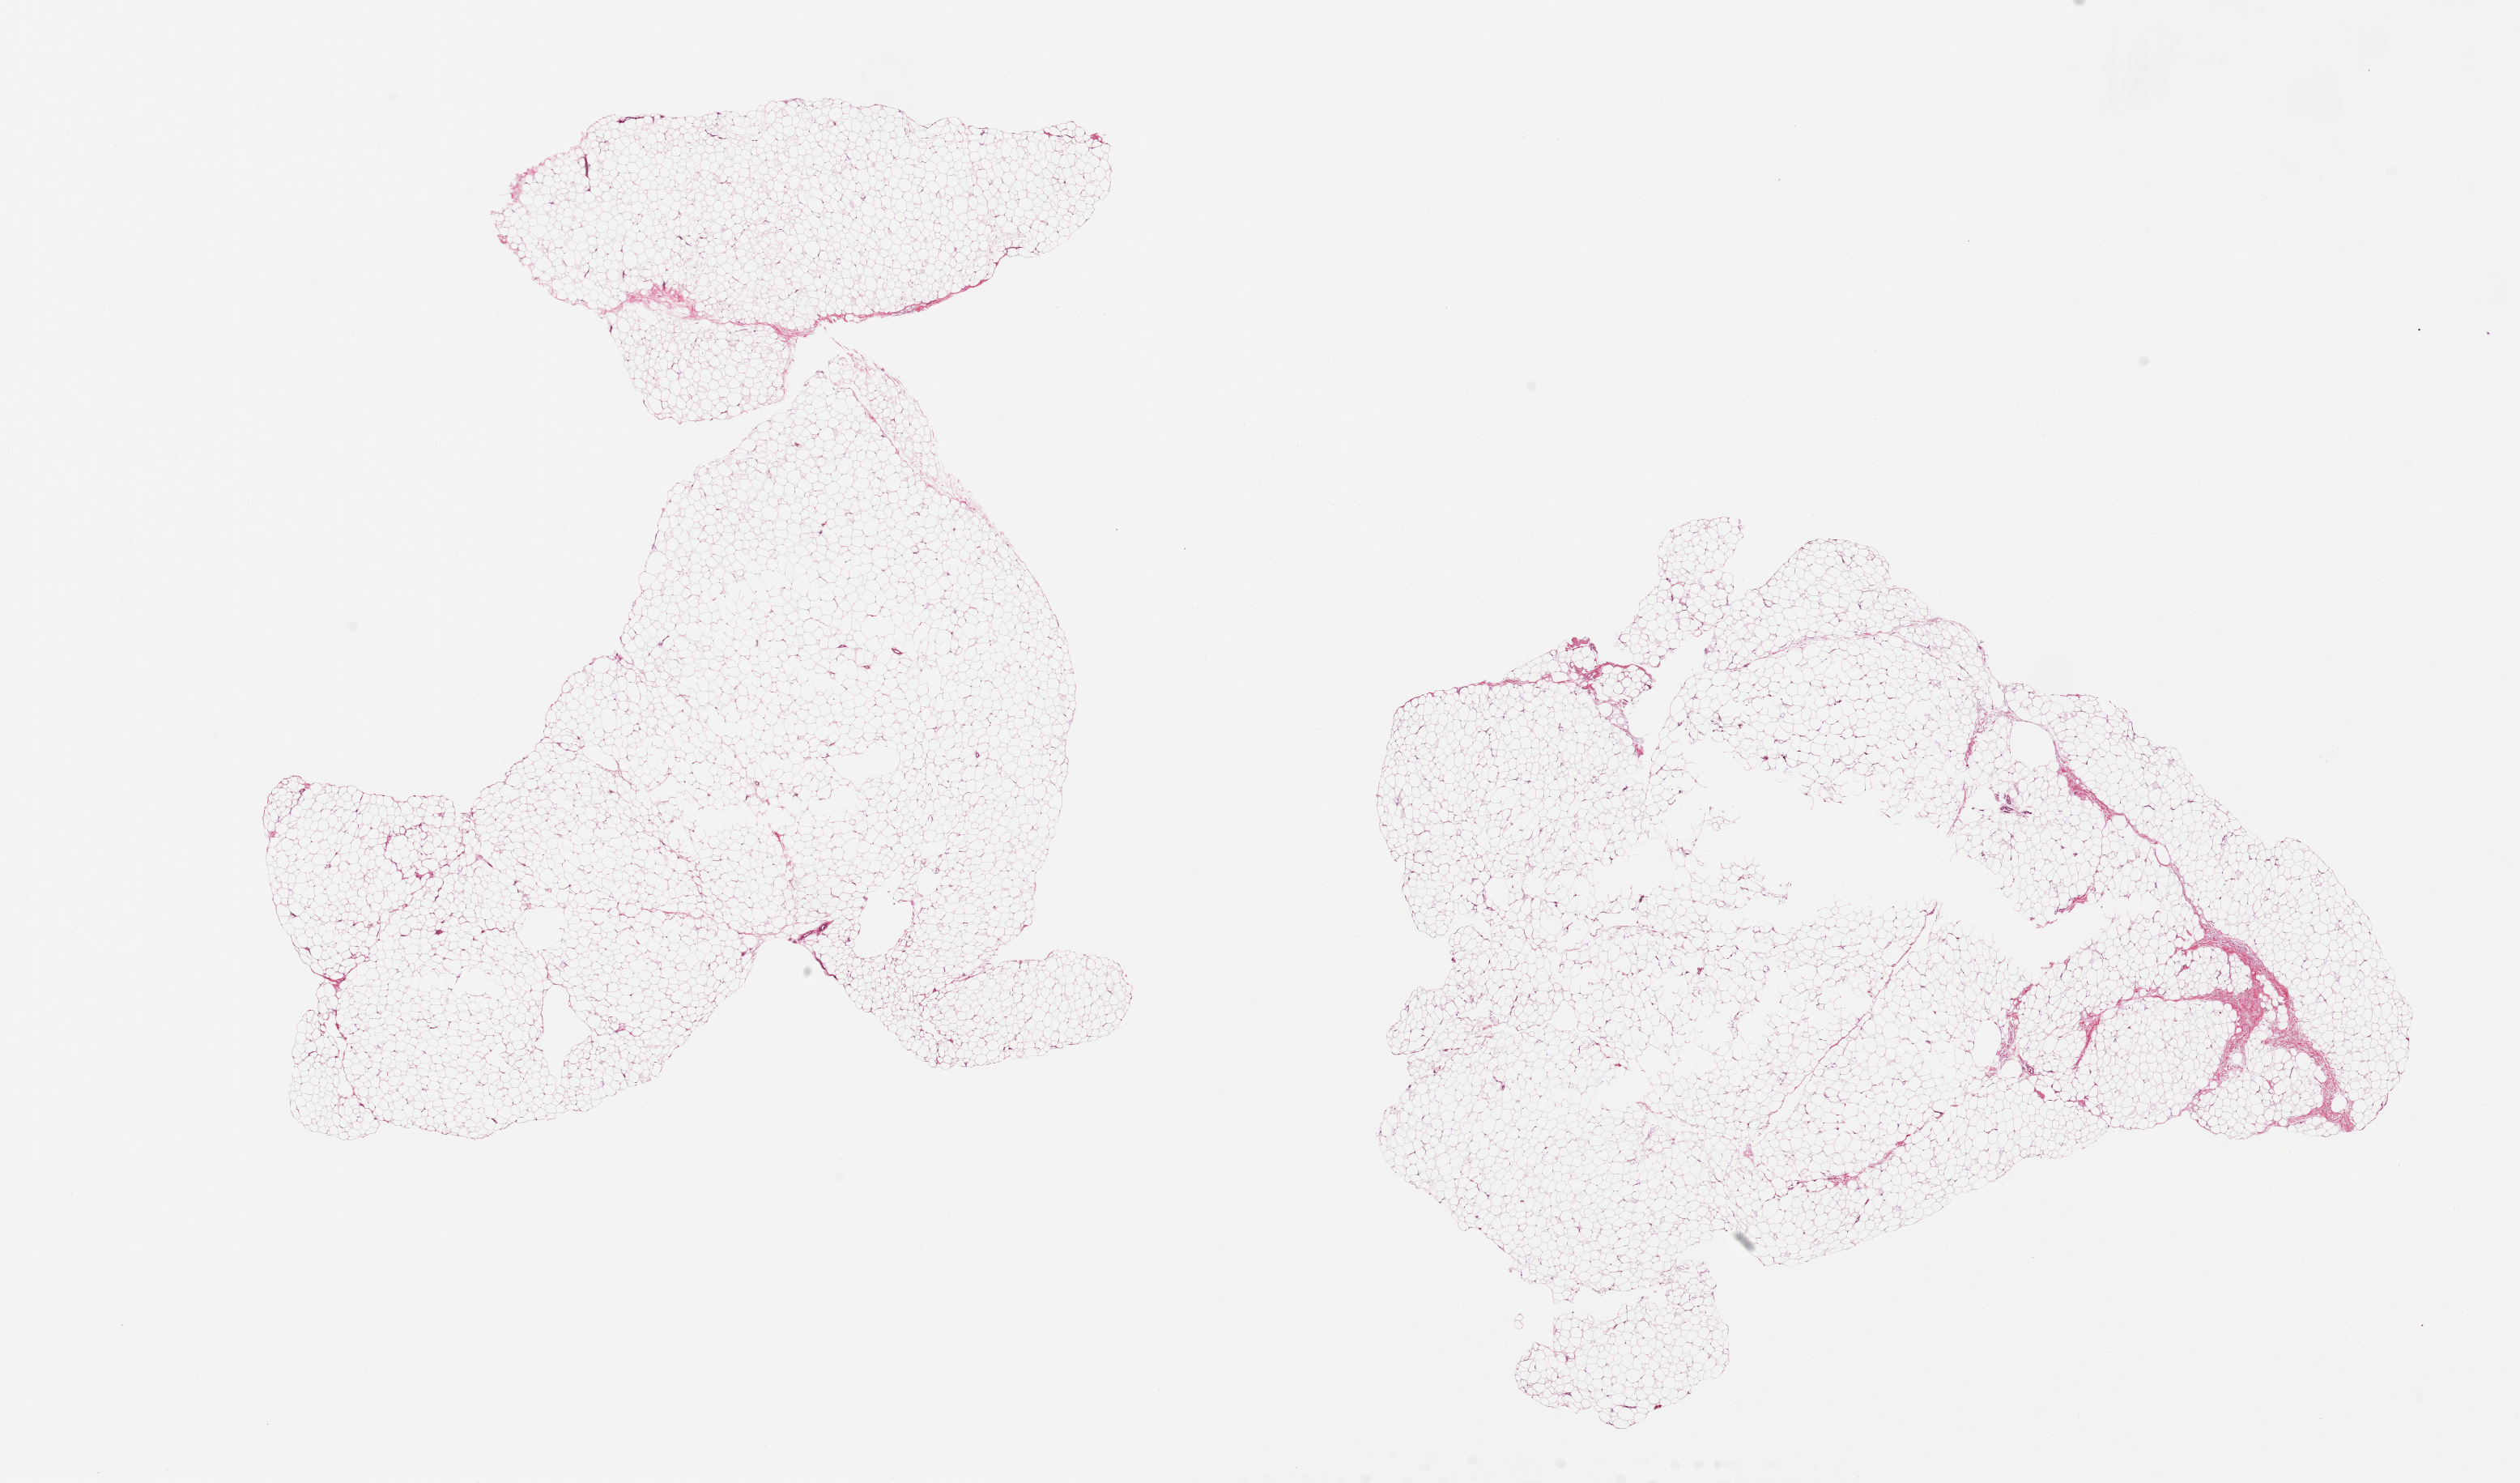
Whole-slide image, hematoxylin and eosin (H&E) stain — a low-resolution overview of the entire scanned area, about 24.6 x 14.5 mm. PAXgene-fixed paraffin-embedded (PFPE) section. Section of adipose tissue (target tissue). Donor tissue sample. Donor sex: male.
- reviewer comment on this tissue sample: 2 pieces ~9x8mm